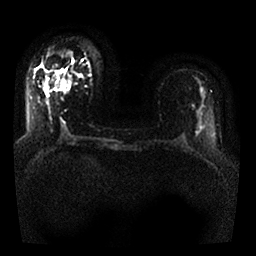
Breast MRI, one axial slice. Slice 13 of 25 in the series (ordered by position). Diffusion-weighted series; image 2 of 4 stored at this slice position (different b-values; order by instance number). 1.5 T. 256 × 256 image matrix, field of view 330 × 330 mm. Female patient.
Structures marked on this image (outlined manually by an expert reader):
- tumour on diffusion-weighted imaging: bounding box (x1, y1, x2, y2) in pixels: (60, 82, 63, 87)